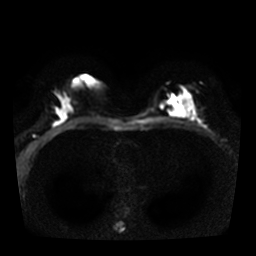
Breast MRI, one axial slice. Slice 16 of 36 in the series (ordered by position). Diffusion-weighted series; image 2 of 4 stored at this slice position (different b-values; order by instance number). 3 T. 5 mm slice thickness. 256 × 256 image matrix, field of view 320 × 320 mm. Female patient.
Outlined on this slice (outlined manually by an expert reader):
- tumour on diffusion-weighted imaging: box from (x=168, y=91) to (x=193, y=117) px